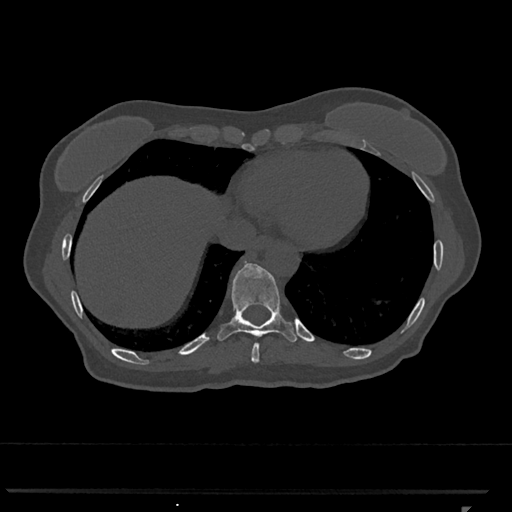
CT including the spine, one axial slice. Reconstruction kernel Br40s/3. Bone window (W 1800 / L 400 HU). 0.5 mm slice thickness. 512 × 512 image matrix. Female patient, age 62 years. From the clinical record (not read from this slice): primary cancer: renal.
Outlined on this slice (semi-automatic segmentation, software-assisted and operator-edited):
- T10 vertebra: bounding box [x1, y1, x2, y2] px = [217, 261, 297, 345]
- T9 vertebra: [251, 343, 259, 363]